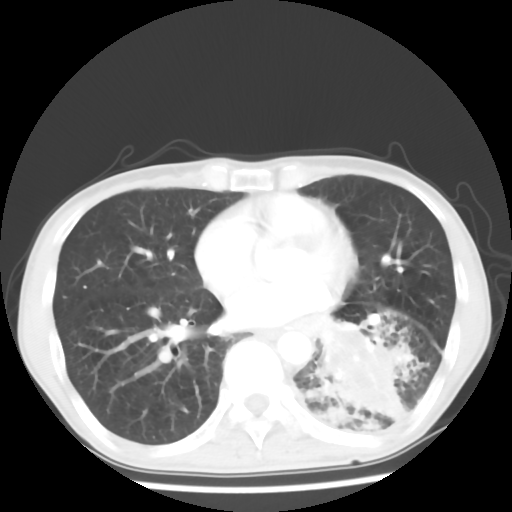
Chest CT, one axial slice. Position 26 of 64 along the scan axis. Lung window (W 1500 / L -600 HU). 512 × 512 image matrix, field of view 313 × 313 mm. Male patient, age 68 years. Case-level facts recorded for this patient, not image findings: clinical TNM (as recorded): T4 N0 M0.
Annotated regions visible in this slice (bounding box drawn by a radiologist):
- lung tumour (recorded histology: squamous cell carcinoma): bounding box <301,311,409,437> (left, top, right, bottom; pixels)